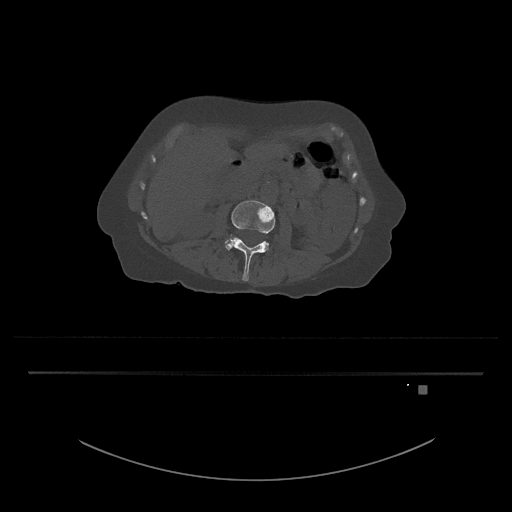
CT including the spine, one axial slice. Slice 422 of 797 in the series (ordered by position). Reconstruction kernel Br40s/3. 120 kVp. Bone window (W 1800 / L 400 HU). 512 × 512 image matrix, field of view 500 × 500 mm. Patient: female, 57 years. From the clinical record (not read from this slice): primary cancer: cervical.
Structures marked on this image (semi-automatically segmented with operator editing):
- L3 vertebra: box from (x=225, y=200) to (x=275, y=281) px
- L4 vertebra: (x=225, y=240)–(x=228, y=243)